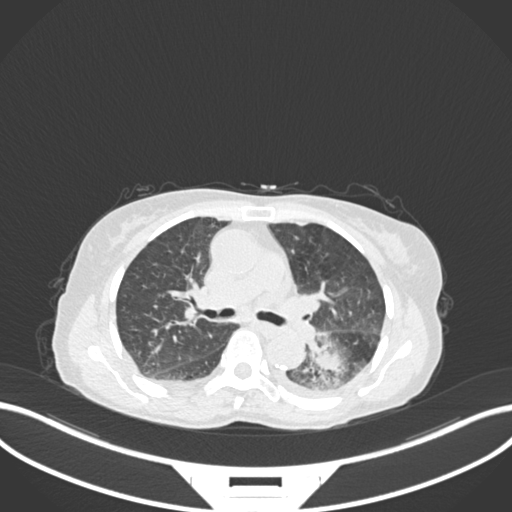
Chest CT, one axial slice; position 107 of 233 along the scan axis; 120 kVp; lung window (W 1500 / L -600 HU); 512 × 512 image matrix, field of view 400 × 400 mm. Female patient, age 78 years. Case-level facts recorded for this patient, not image findings: clinical TNM (as recorded): T3 N0 M1.
Structures marked on this image (bounding box drawn by a radiologist):
- lung tumour (recorded histology: squamous cell carcinoma): bounding box <298,328,354,386> (left, top, right, bottom; pixels)